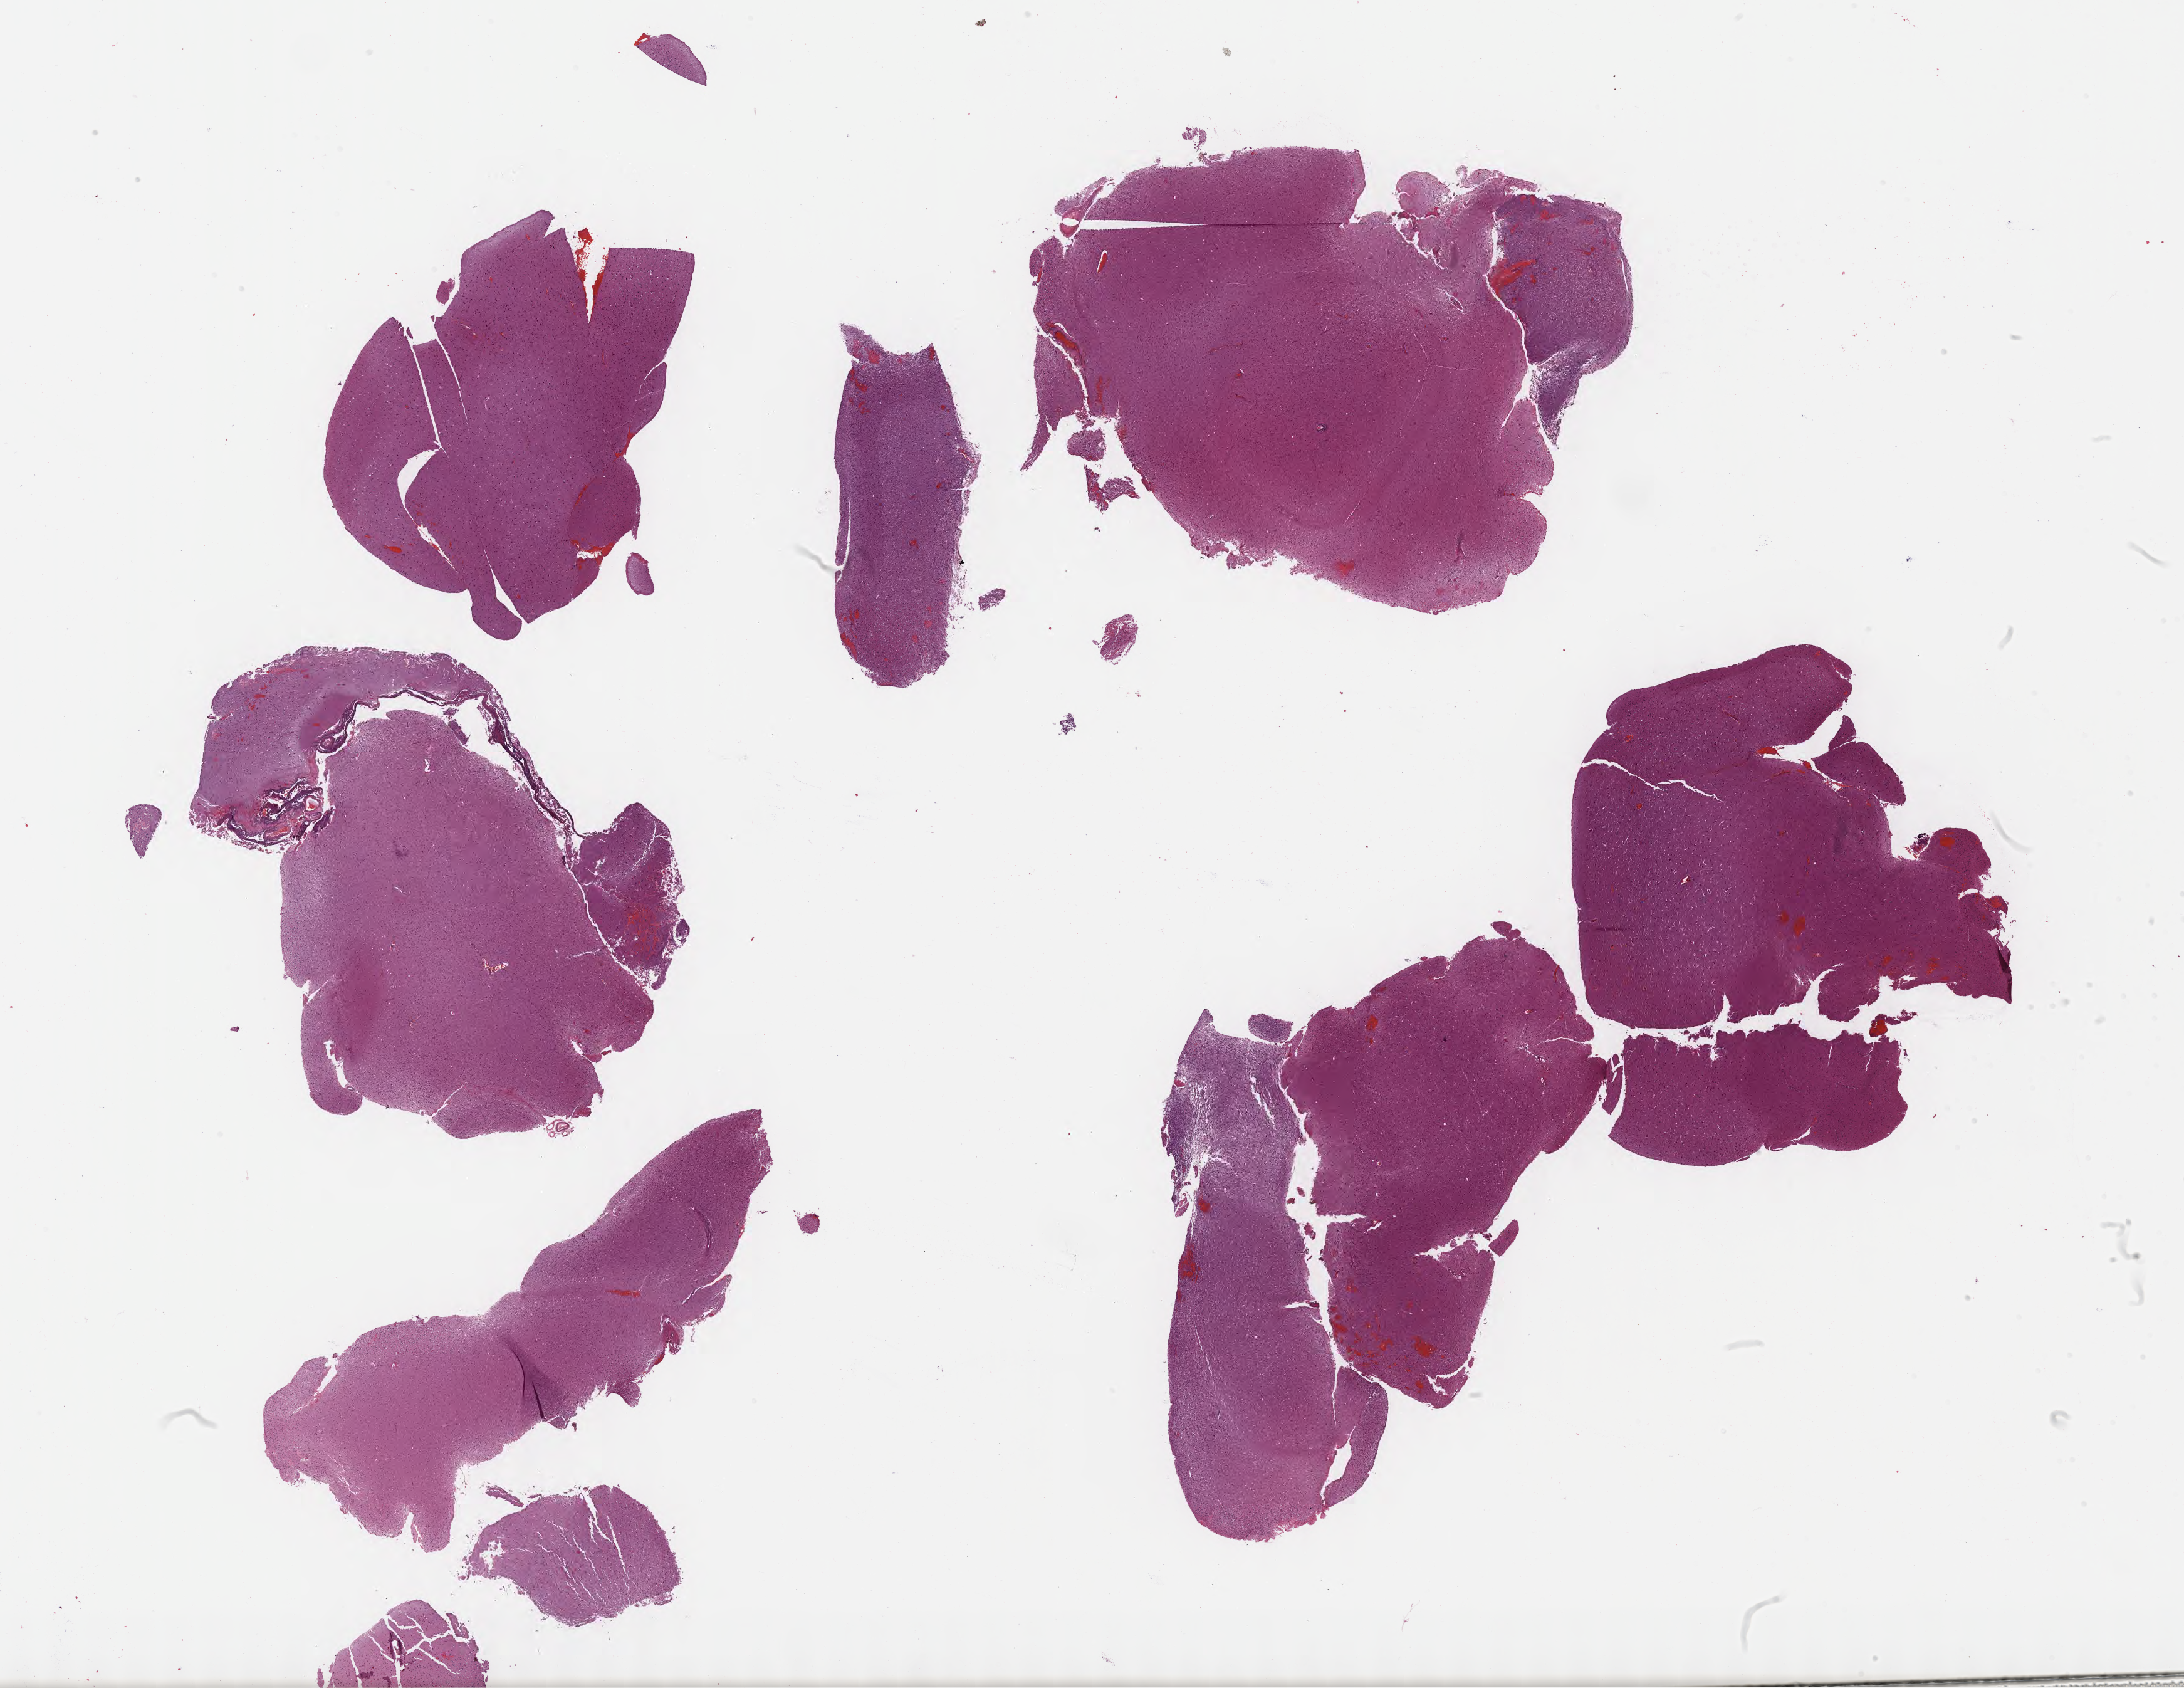
Digitized H&E-stained tissue section (whole slide) — low-resolution overview of the scanned area, about 28.2 x 21.8 mm (slide scanned at 40x). Formalin-fixed paraffin-embedded (FFPE) diagnostic section. Brain, primary tumour sample. Male patient; age at initial diagnosis 38 years.
Pathologic diagnosis: Oligodendroglioma, NOS.